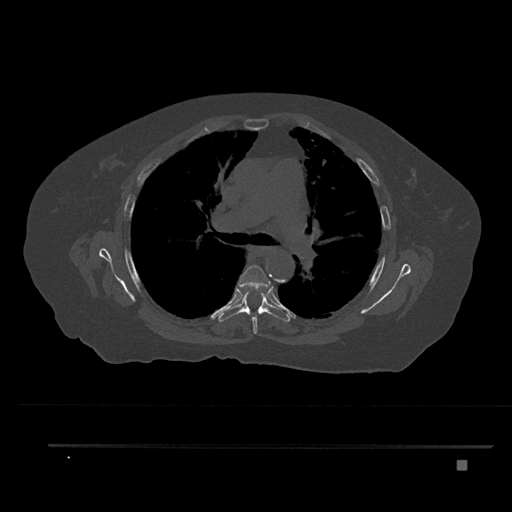
CT including the spine, one axial slice. Slice 544 of 797 in the series (ordered by position). 120 kVp. Bone window (W 1800 / L 400 HU). 512 × 512 image matrix, field of view 437 × 437 mm. Patient: female, 76 years. From the clinical record (not read from this slice): primary cancer: lung; vertebrae with lytic lesions (as recorded): T11, L3.
Annotated regions visible in this slice (semi-automatic segmentation, software-assisted and operator-edited):
- T5 vertebra: bounding box [x1, y1, x2, y2] px = [238, 265, 270, 334]
- T6 vertebra: [218, 290, 290, 322]